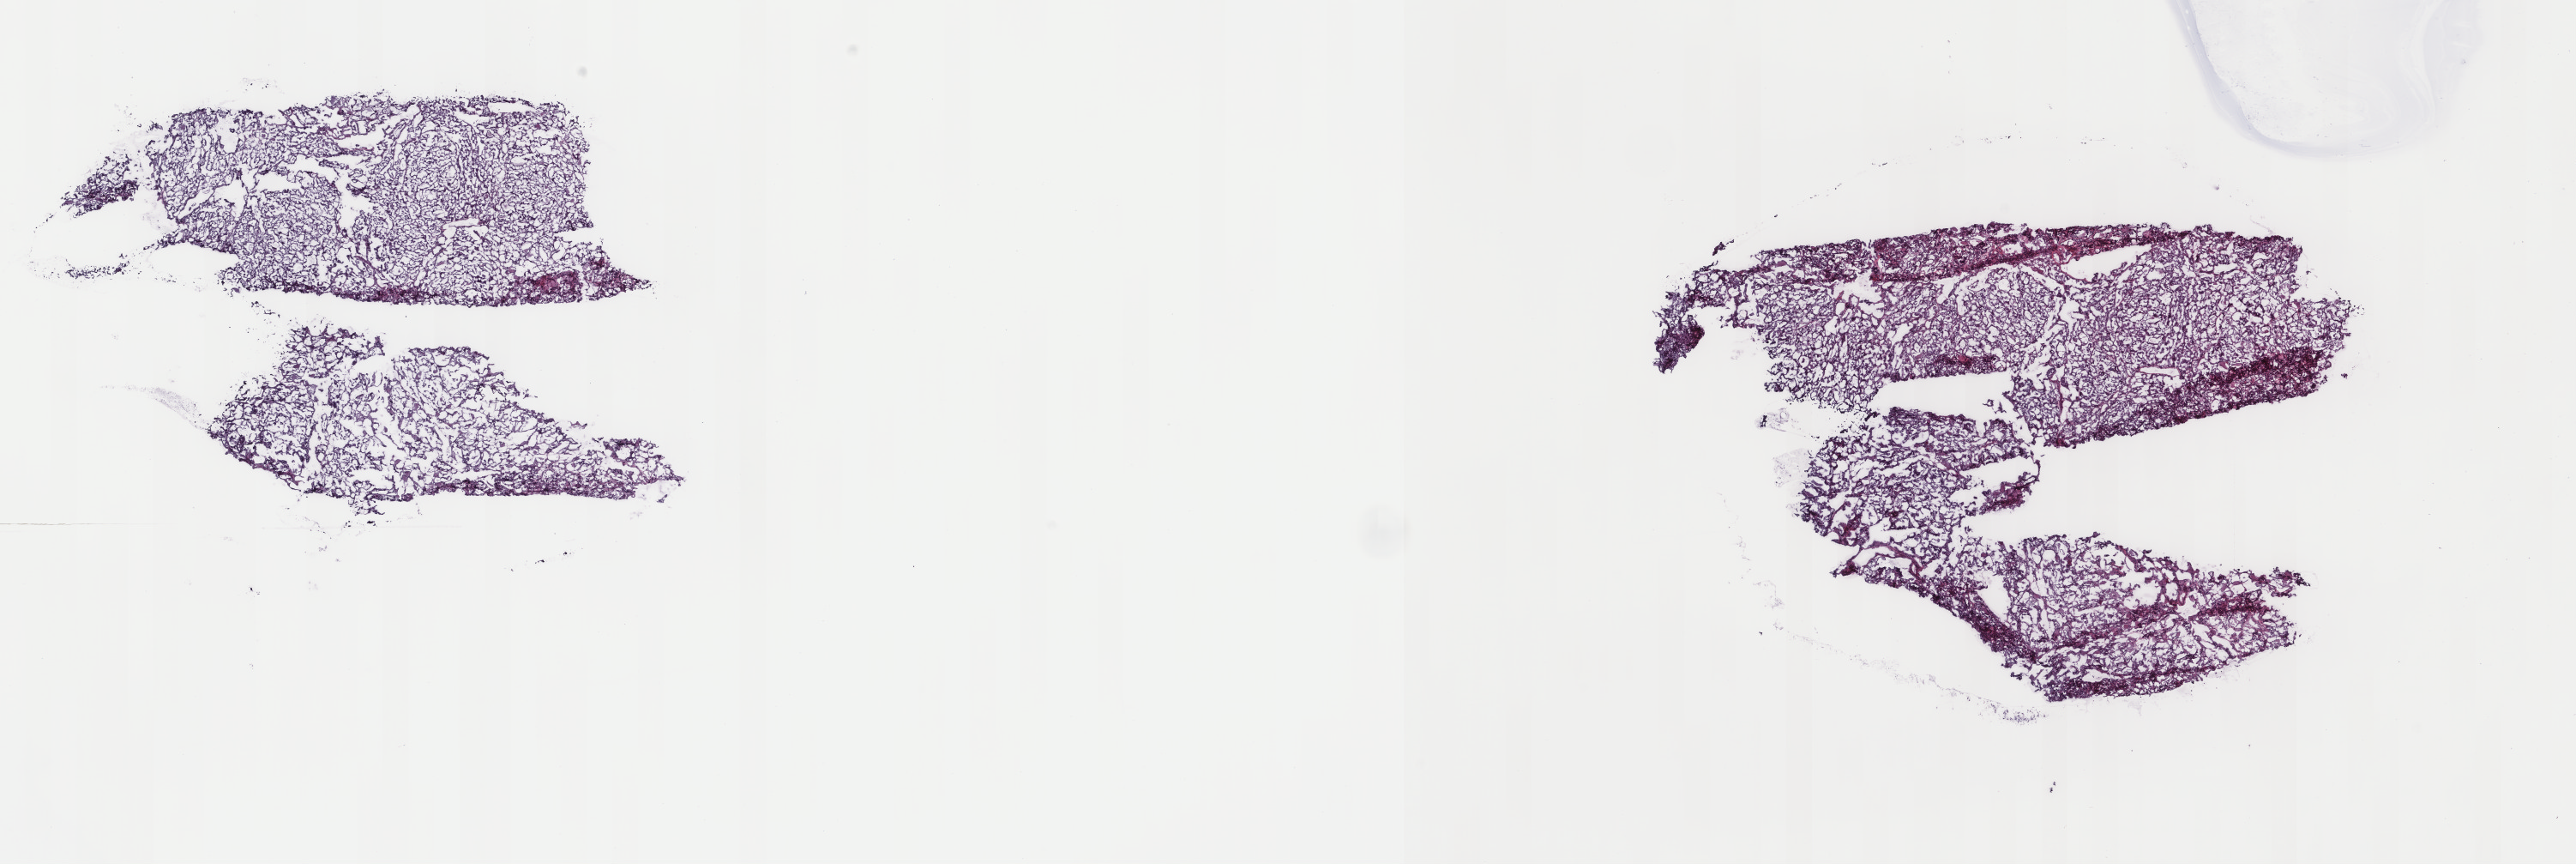
Digitized H&E tissue section (whole slide) — whole scanned area (about 23.8 x 8.0 mm, slide scanned at 40x) shown as a low-resolution overview. Frozen section from the top of the tissue portion. Thyroid, primary tumour sample. Female patient; age at initial diagnosis 31 years. Composition of this section per pathologist review: tumour cells 95%, tumour nuclei 100%, normal cells 0%, stromal cells 5%, necrosis 0%. Inflammatory infiltration, as recorded: lymphocyte infiltration 0%, monocyte infiltration 1%, neutrophil infiltration 0%.
Laterality: right. Lymph nodes positive (case pathology): 0 of 4 examined. AJCC pathologic stage: I. TNM: T2 N0 M0. Histologic diagnosis: Papillary adenocarcinoma, NOS (thyroid gland).